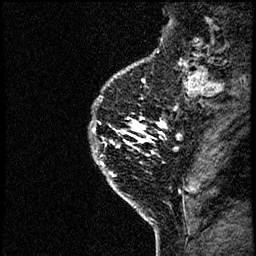
Breast MRI (dynamic contrast-enhanced), one sagittal slice; slice 53 of 60 in the series (ordered by position); dynamic contrast-enhanced study with each time point stored as its own series, time point 2 of 4 at this slice position (early post-contrast, ordered by acquisition time); 1.5 T; TE 4.2 ms, TR 17.6 ms; 2 mm slice thickness; 256 × 256 image matrix, field of view 200 × 200 mm. Patient: female, 40 years. Case-level facts recorded for this patient, not image findings: setting: breast cancer imaged before/during neoadjuvant chemotherapy; receptor status: HER2-positive.
Structures marked on this image (semi-automatically segmented with operator editing):
- analysis volume of interest (the breast-tissue region the enhancement analysis was run in; not a lesion): box from (x=83, y=55) to (x=185, y=206) px
- tumour enhancement mask (voxels above the 100 % enhancement threshold inside the analysis volume of interest): (x=94, y=118)–(x=161, y=205)